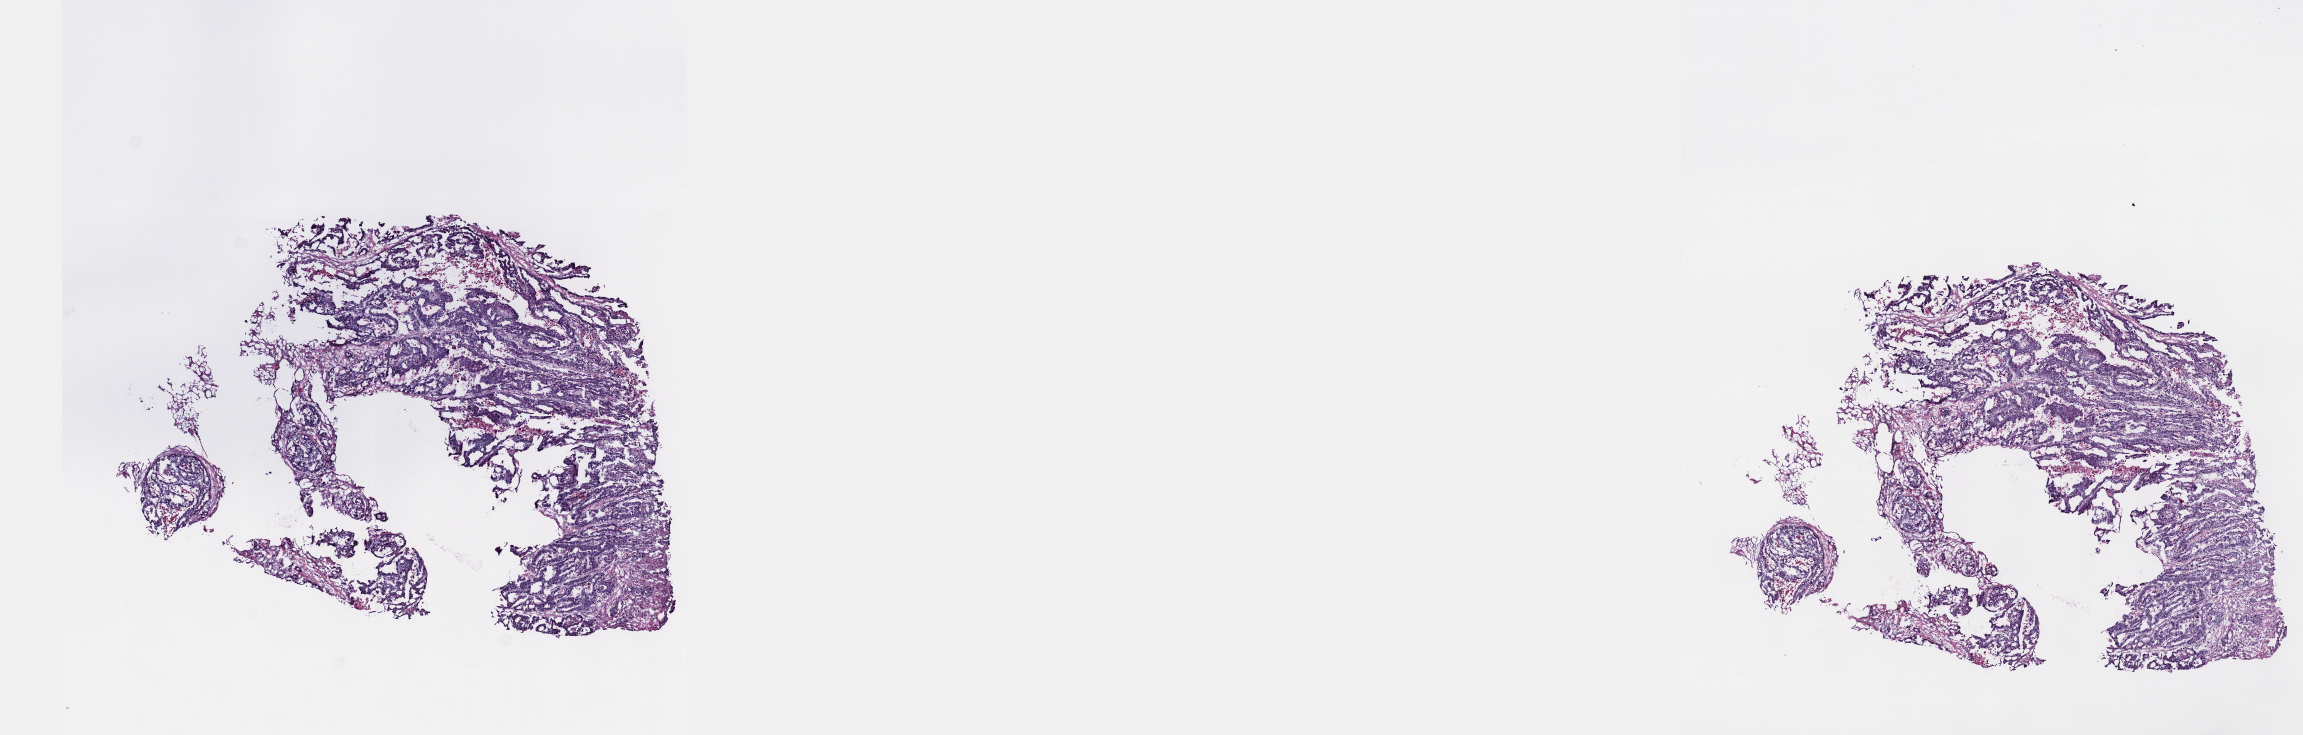
Whole-slide histology image, Hematoxylin and eosin (H&E) stained — low-resolution overview of the scanned area, about 18.6 x 5.9 mm (slide scanned at 40x). Frozen section. Stomach, primary tumour sample. Patient: female, age at initial diagnosis 79 years. Histologic grade: G1 (well differentiated). Composition of this section per pathologist review: tumour cells 60%, tumour nuclei 70%, normal cells 0%, stromal cells 40%, necrosis 0%. Inflammatory infiltration, as recorded: lymphocyte infiltration 0%, monocyte infiltration 0%, neutrophil infiltration 0%.
* diagnosis: Tubular adenocarcinoma (body of stomach)
* TNM: T3 N1 M0
* AJCC pathologic stage: IIB (7th edition)